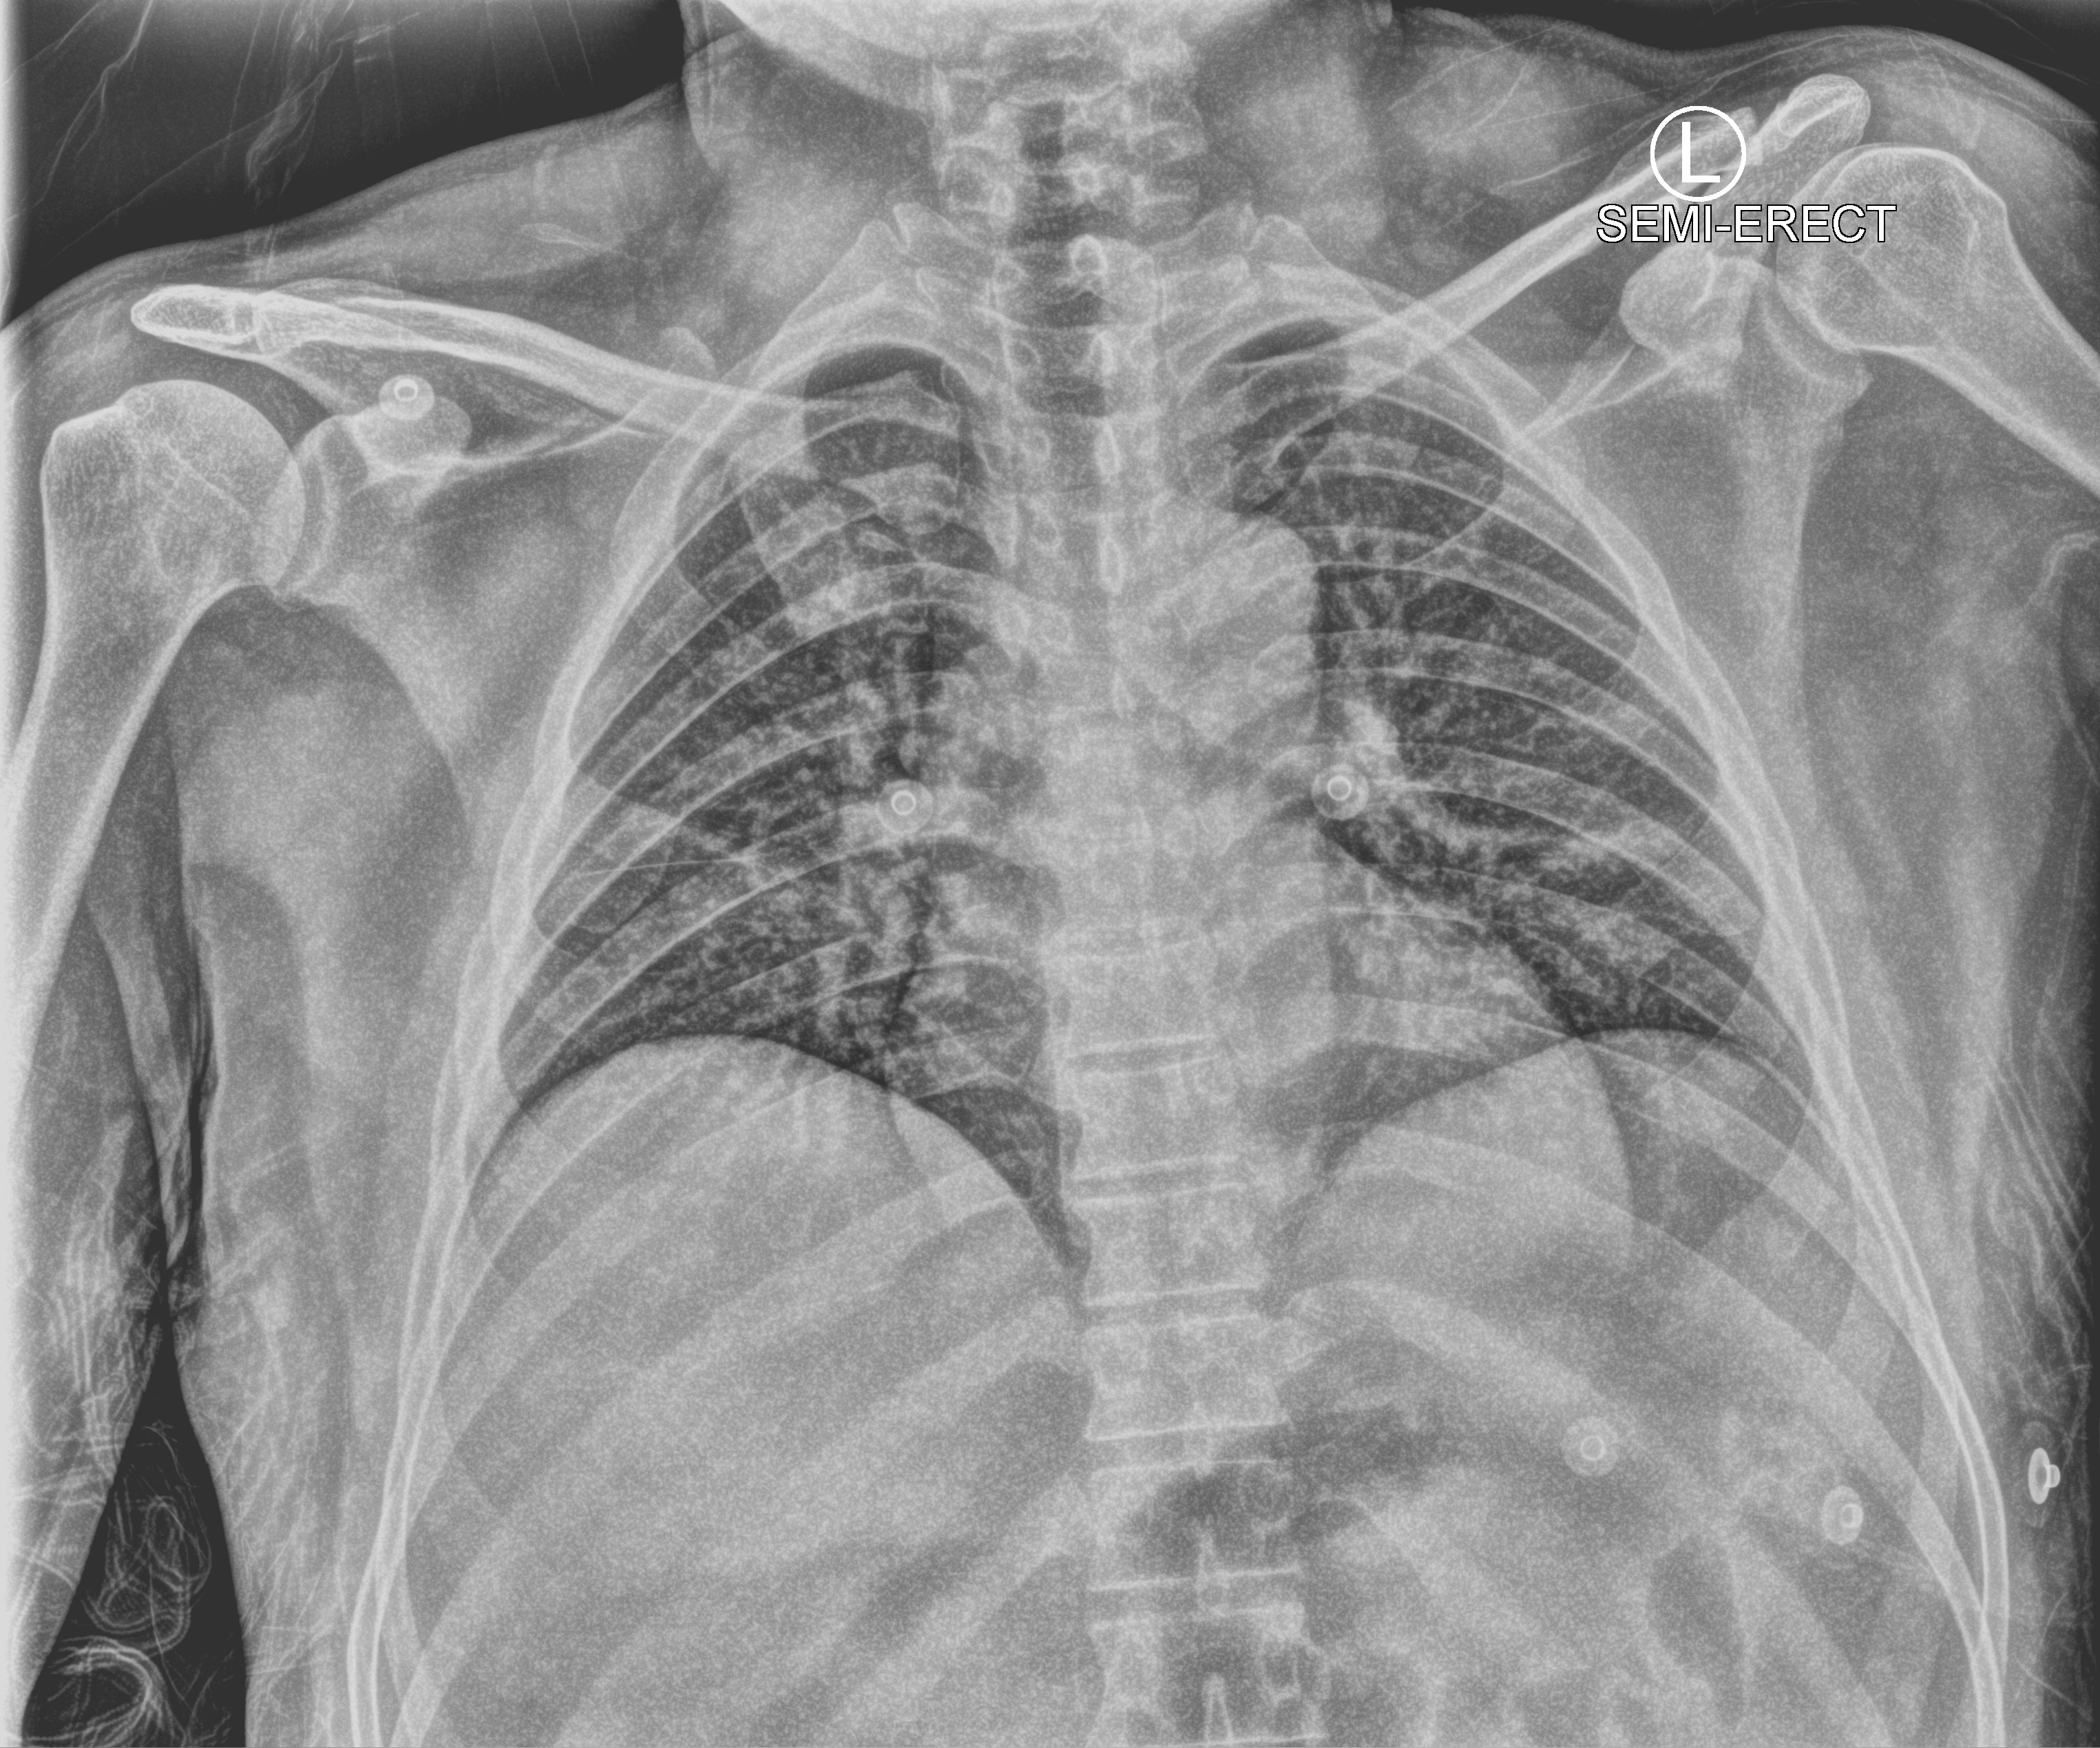
Portable chest radiograph. Patient hospitalised with COVID-19; male, aged 18–59 years.
From the hospital-stay record, not from the radiograph (when in the stay this image was taken is not recorded): admitted to intensive care during this hospital stay: no.